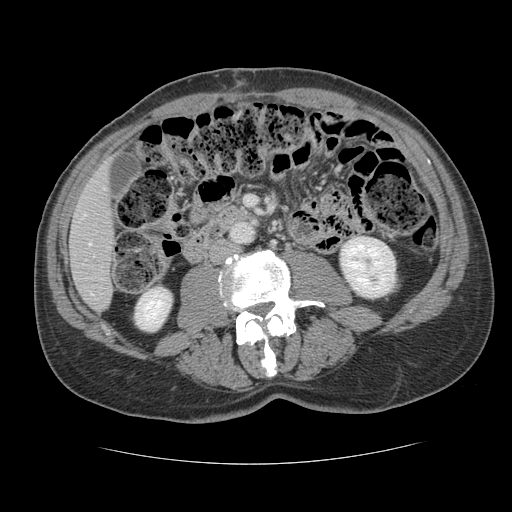
Contrast-enhanced abdominal CT, one axial slice. Position 35 of 134 along the scan axis. Reconstruction kernel STANDARD. Intravenous contrast given. Soft-tissue window (W 400 / L 40 HU). 512 × 512 image matrix, field of view 377 × 377 mm. Male patient, age 68 years. Case-level facts recorded for this patient, not image findings: diagnosis: colorectal cancer liver metastases, imaged before liver resection; multiple liver metastases: yes; largest metastasis: 2.2 cm; disease in both lobes: no.
Annotated regions visible in this slice (expert manual segmentation):
- hepatic veins: bounding box <89,243,92,245> (left, top, right, bottom; pixels)
- liver: <71,168,115,310>
- planned liver remnant (the part of the liver to remain after resection): <71,168,115,310>